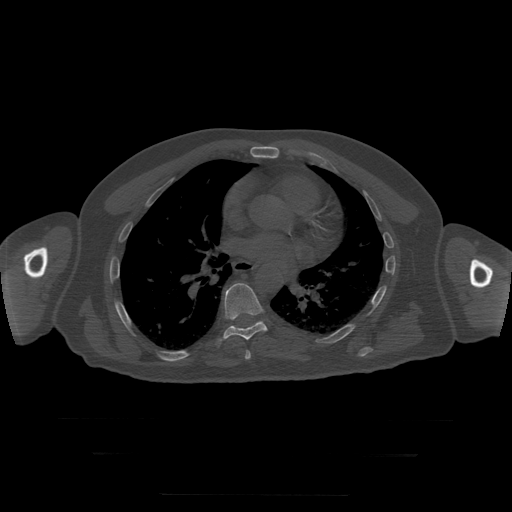
CT including the spine, one axial slice; reconstruction kernel STANDARD; 120 kVp; bone window (W 1800 / L 400 HU); 1.25 mm slice thickness; 512 × 512 image matrix. Patient age 73 years. Case-level facts recorded for this patient, not image findings: primary cancer: prostate.
Outlined on this slice (semi-automatic segmentation, software-assisted and operator-edited):
- T7 vertebra: bounding box <245,351,251,360> (left, top, right, bottom; pixels)
- T8 vertebra: <215,283,277,346>